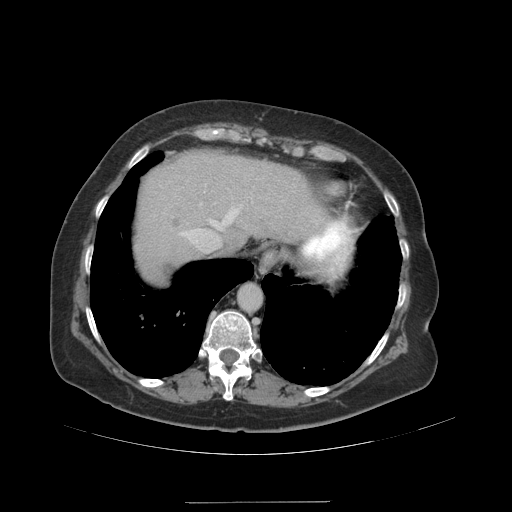
Contrast-enhanced abdominal CT (liver protocol), one axial slice; slice 82 of 99 in the series (ordered by position); reconstruction kernel STANDARD; 140 kVp; soft-tissue window (W 400 / L 40 HU); 512 × 512 image matrix. Case-level facts recorded for this patient, not image findings: diagnosis: hepatocellular carcinoma (patient treated with transarterial chemoembolisation; whether this scan precedes or follows treatment is not stated here); TNM stage (as recorded): Stage-IVA; Child-Pugh class: A.
Structures marked on this image (semi-automatically segmented with operator editing):
- abdominal aorta: bounding box (x1, y1, x2, y2) in pixels: (239, 285, 261, 311)
- liver parenchyma outside the tumour (the mass and vessels are separate outlines, so this box may not span the whole liver): (134, 150, 325, 280)
- liver vessels: (179, 204, 242, 252)